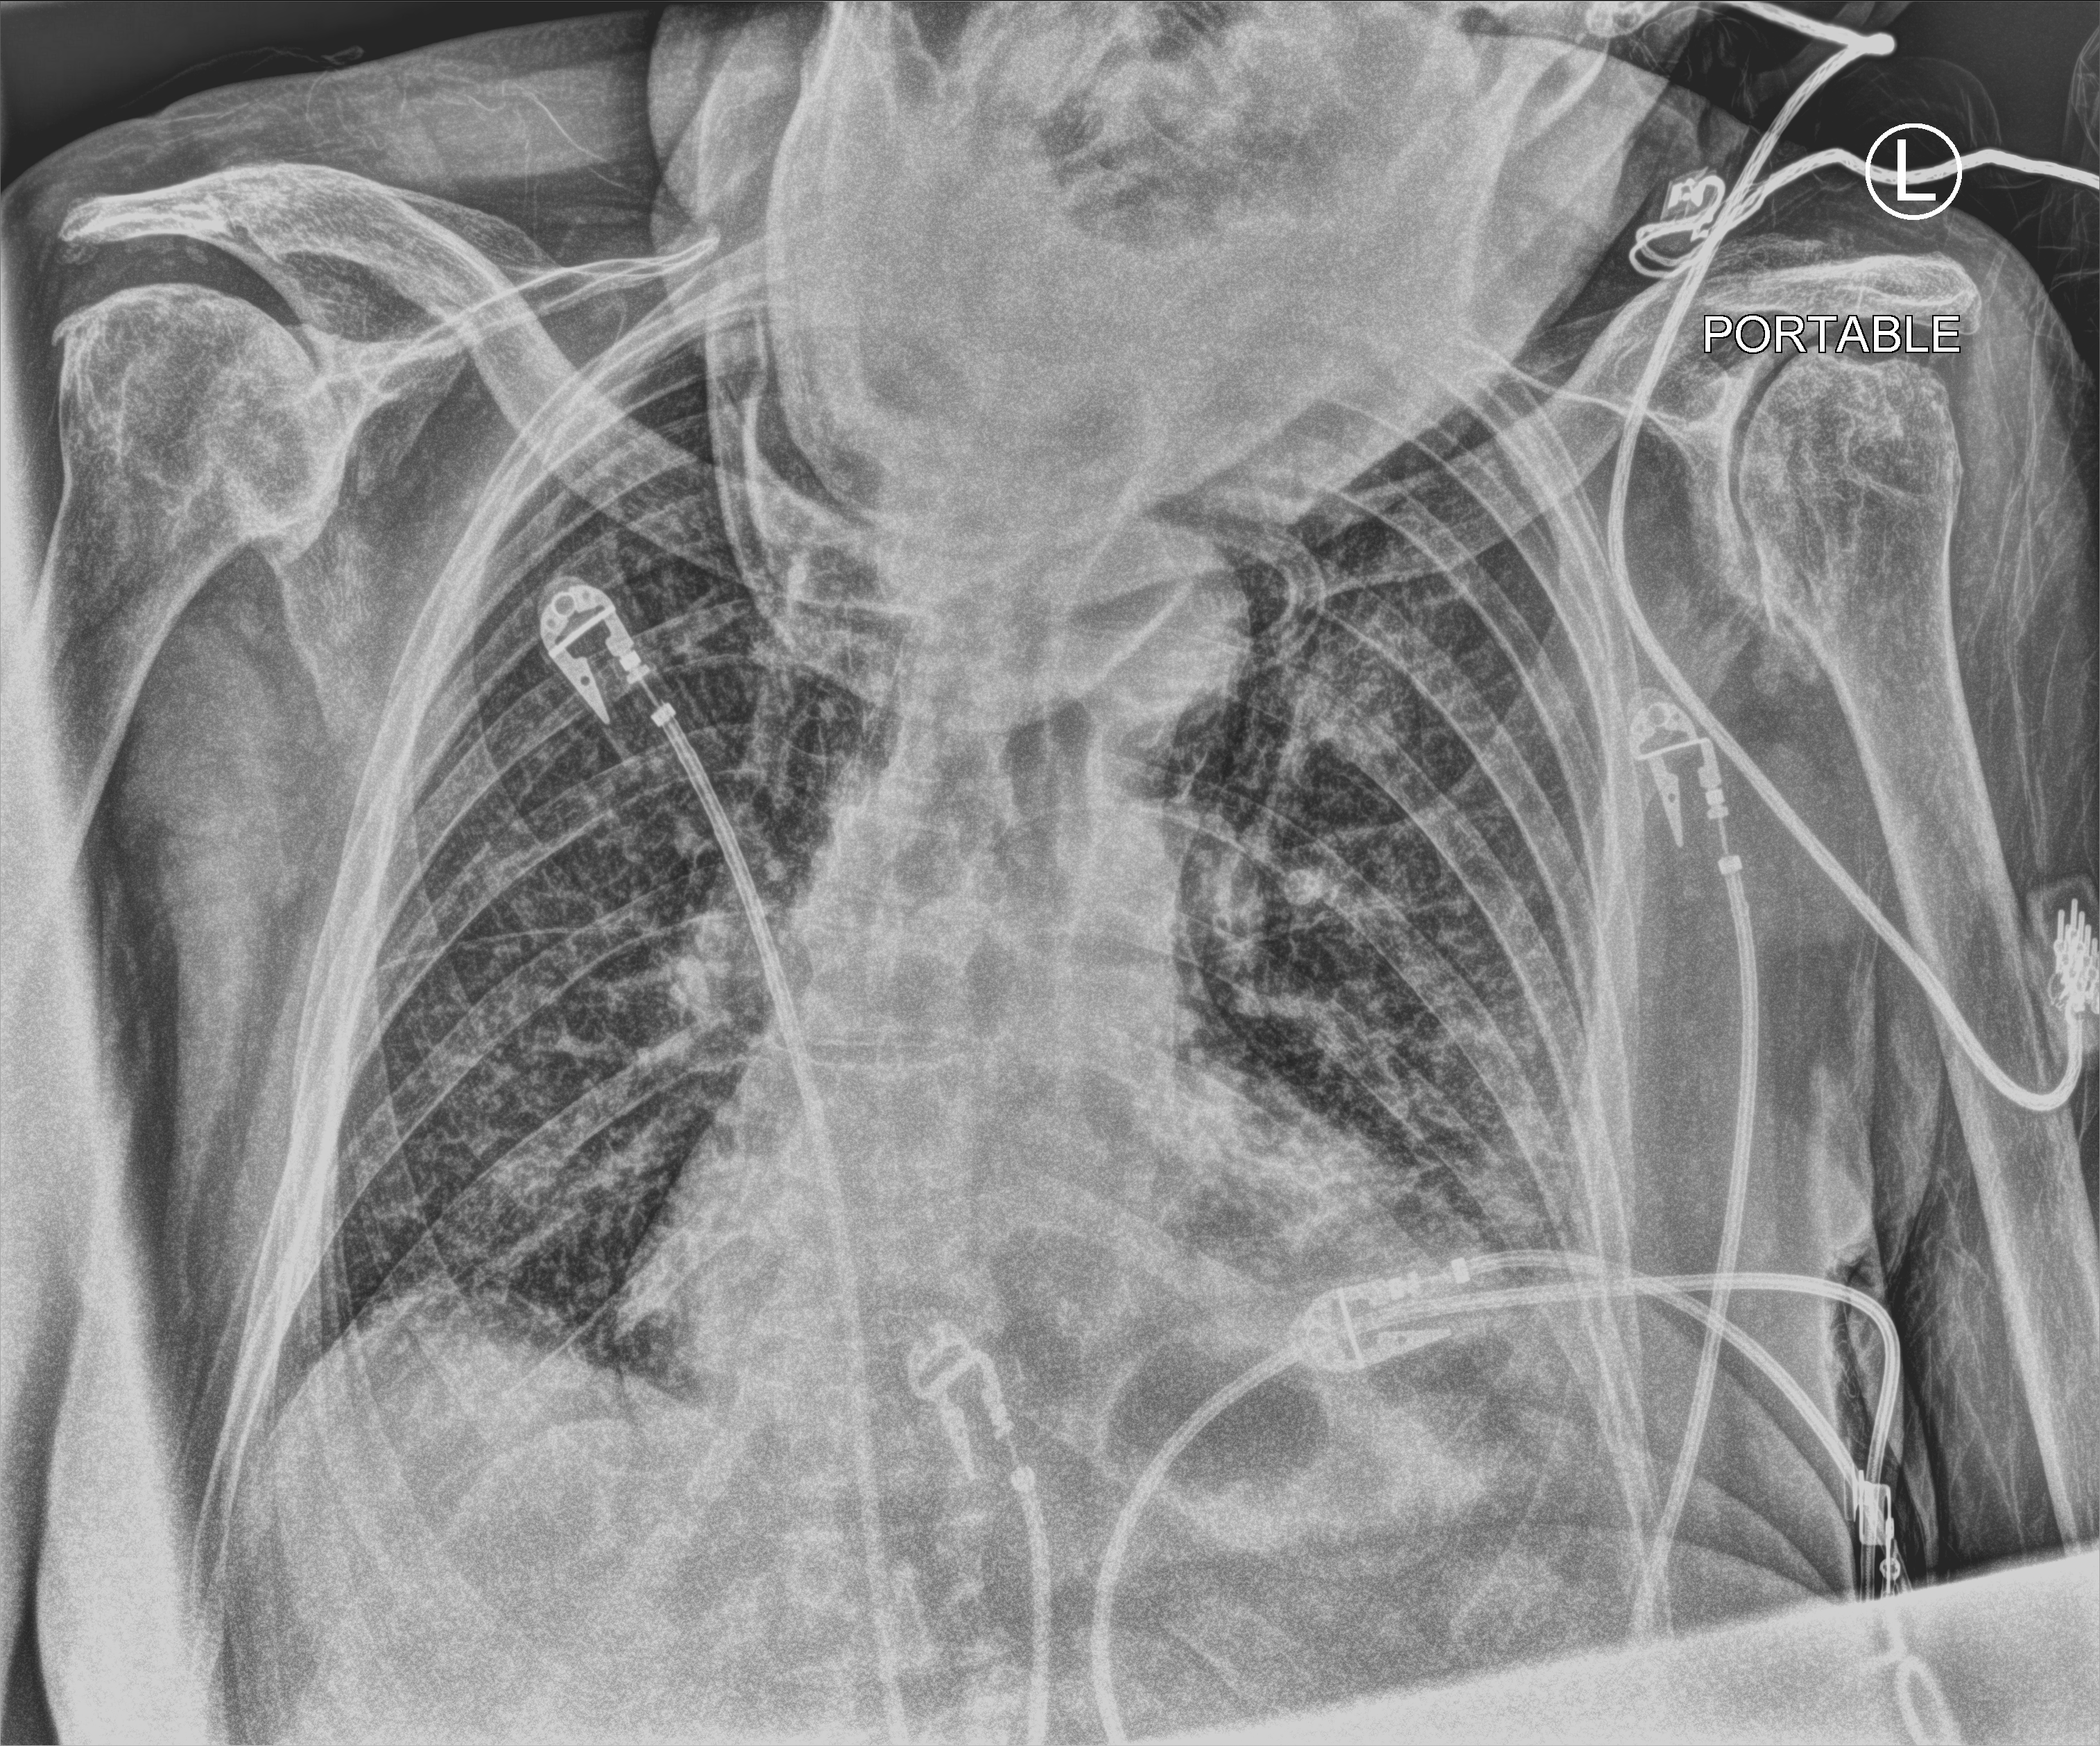
Bedside chest radiograph (computed radiography), anteroposterior (AP) projection. Male patient hospitalised with COVID-19, age 75–90 years.
Hospital-stay facts (about this admission, not read from this image; timing relative to this image not recorded):
- admitted to intensive care during this hospital stay: no
- COPD (admission record): no
- mechanically ventilated during this hospital stay: no